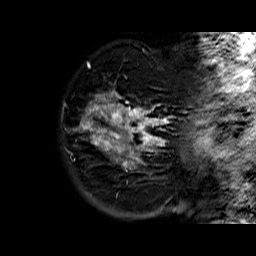
Breast MRI (dynamic contrast-enhanced), one sagittal slice; dynamic contrast-enhanced series, time point 2 of 6 at this slice position (early post-contrast); 1.5 T; TE 6.3 ms, TR 32.4 ms; 4 mm slice thickness; 256 × 256 image matrix, field of view 200 × 200 mm. Female patient. From the clinical record (not read from this slice): setting: breast cancer imaged before/during neoadjuvant chemotherapy; receptor status: HR-positive, HER2-negative.
Outlined on this slice (semi-automatically segmented with operator editing):
- analysis volume of interest (the breast-tissue region the enhancement analysis was run in; not a lesion): bounding box <73,74,175,179> (left, top, right, bottom; pixels)
- tumour enhancement mask (voxels above the 100 % enhancement threshold inside the analysis volume of interest): <76,90,170,167>